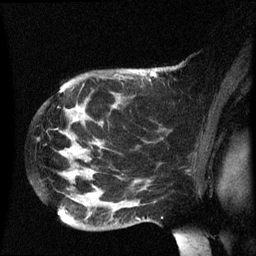
Breast MRI (dynamic contrast-enhanced), one sagittal slice. Slice 45 of 60 in the series (ordered by position). Dynamic contrast-enhanced series, image 2 of 3 at this slice position (ordered by acquisition). 1.5 T. TE 4.2 ms, TR 8.4 ms. 2.5 mm slice thickness. 256 × 256 image matrix, field of view 220 × 220 mm. Patient: female, 49 years.
Outlined on this slice (semi-automatic segmentation, software-assisted and operator-edited):
- analysis volume of interest (the breast-tissue region the enhancement analysis was run in; not a lesion): bounding box <46,72,185,235> (left, top, right, bottom; pixels)
- tumour enhancement mask (voxels above the 70 % enhancement threshold inside the analysis volume of interest): <152,72,156,75>